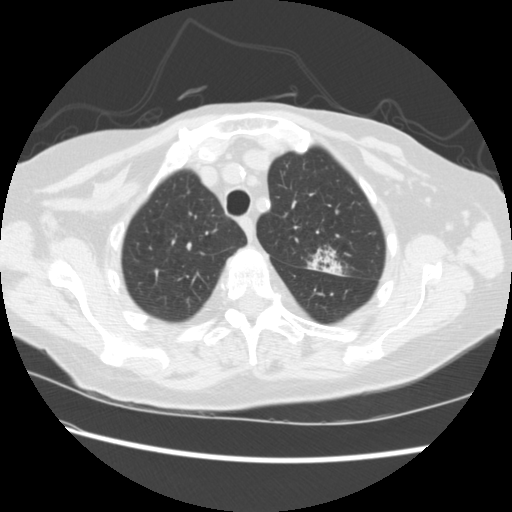
Low-dose screening chest CT, axial slice. First (baseline) screen. Lung window (W 1500 / L -600 HU). Slice 48 of 224 in the series. Female, age 74 years at enrolment. Former smoker at enrolment.
Expert reader's lesion annotation, box from (x=297, y=241) to (x=347, y=282) px. The screening reader recorded 2 non-calcified nodules or masses ≥4 mm on this exam; which of them this box marks is not recorded. Later outcome: lung cancer diagnosed 309 days after this screen — non-small cell carcinoma, left upper lobe, stage IV (AJCC 6th edition).